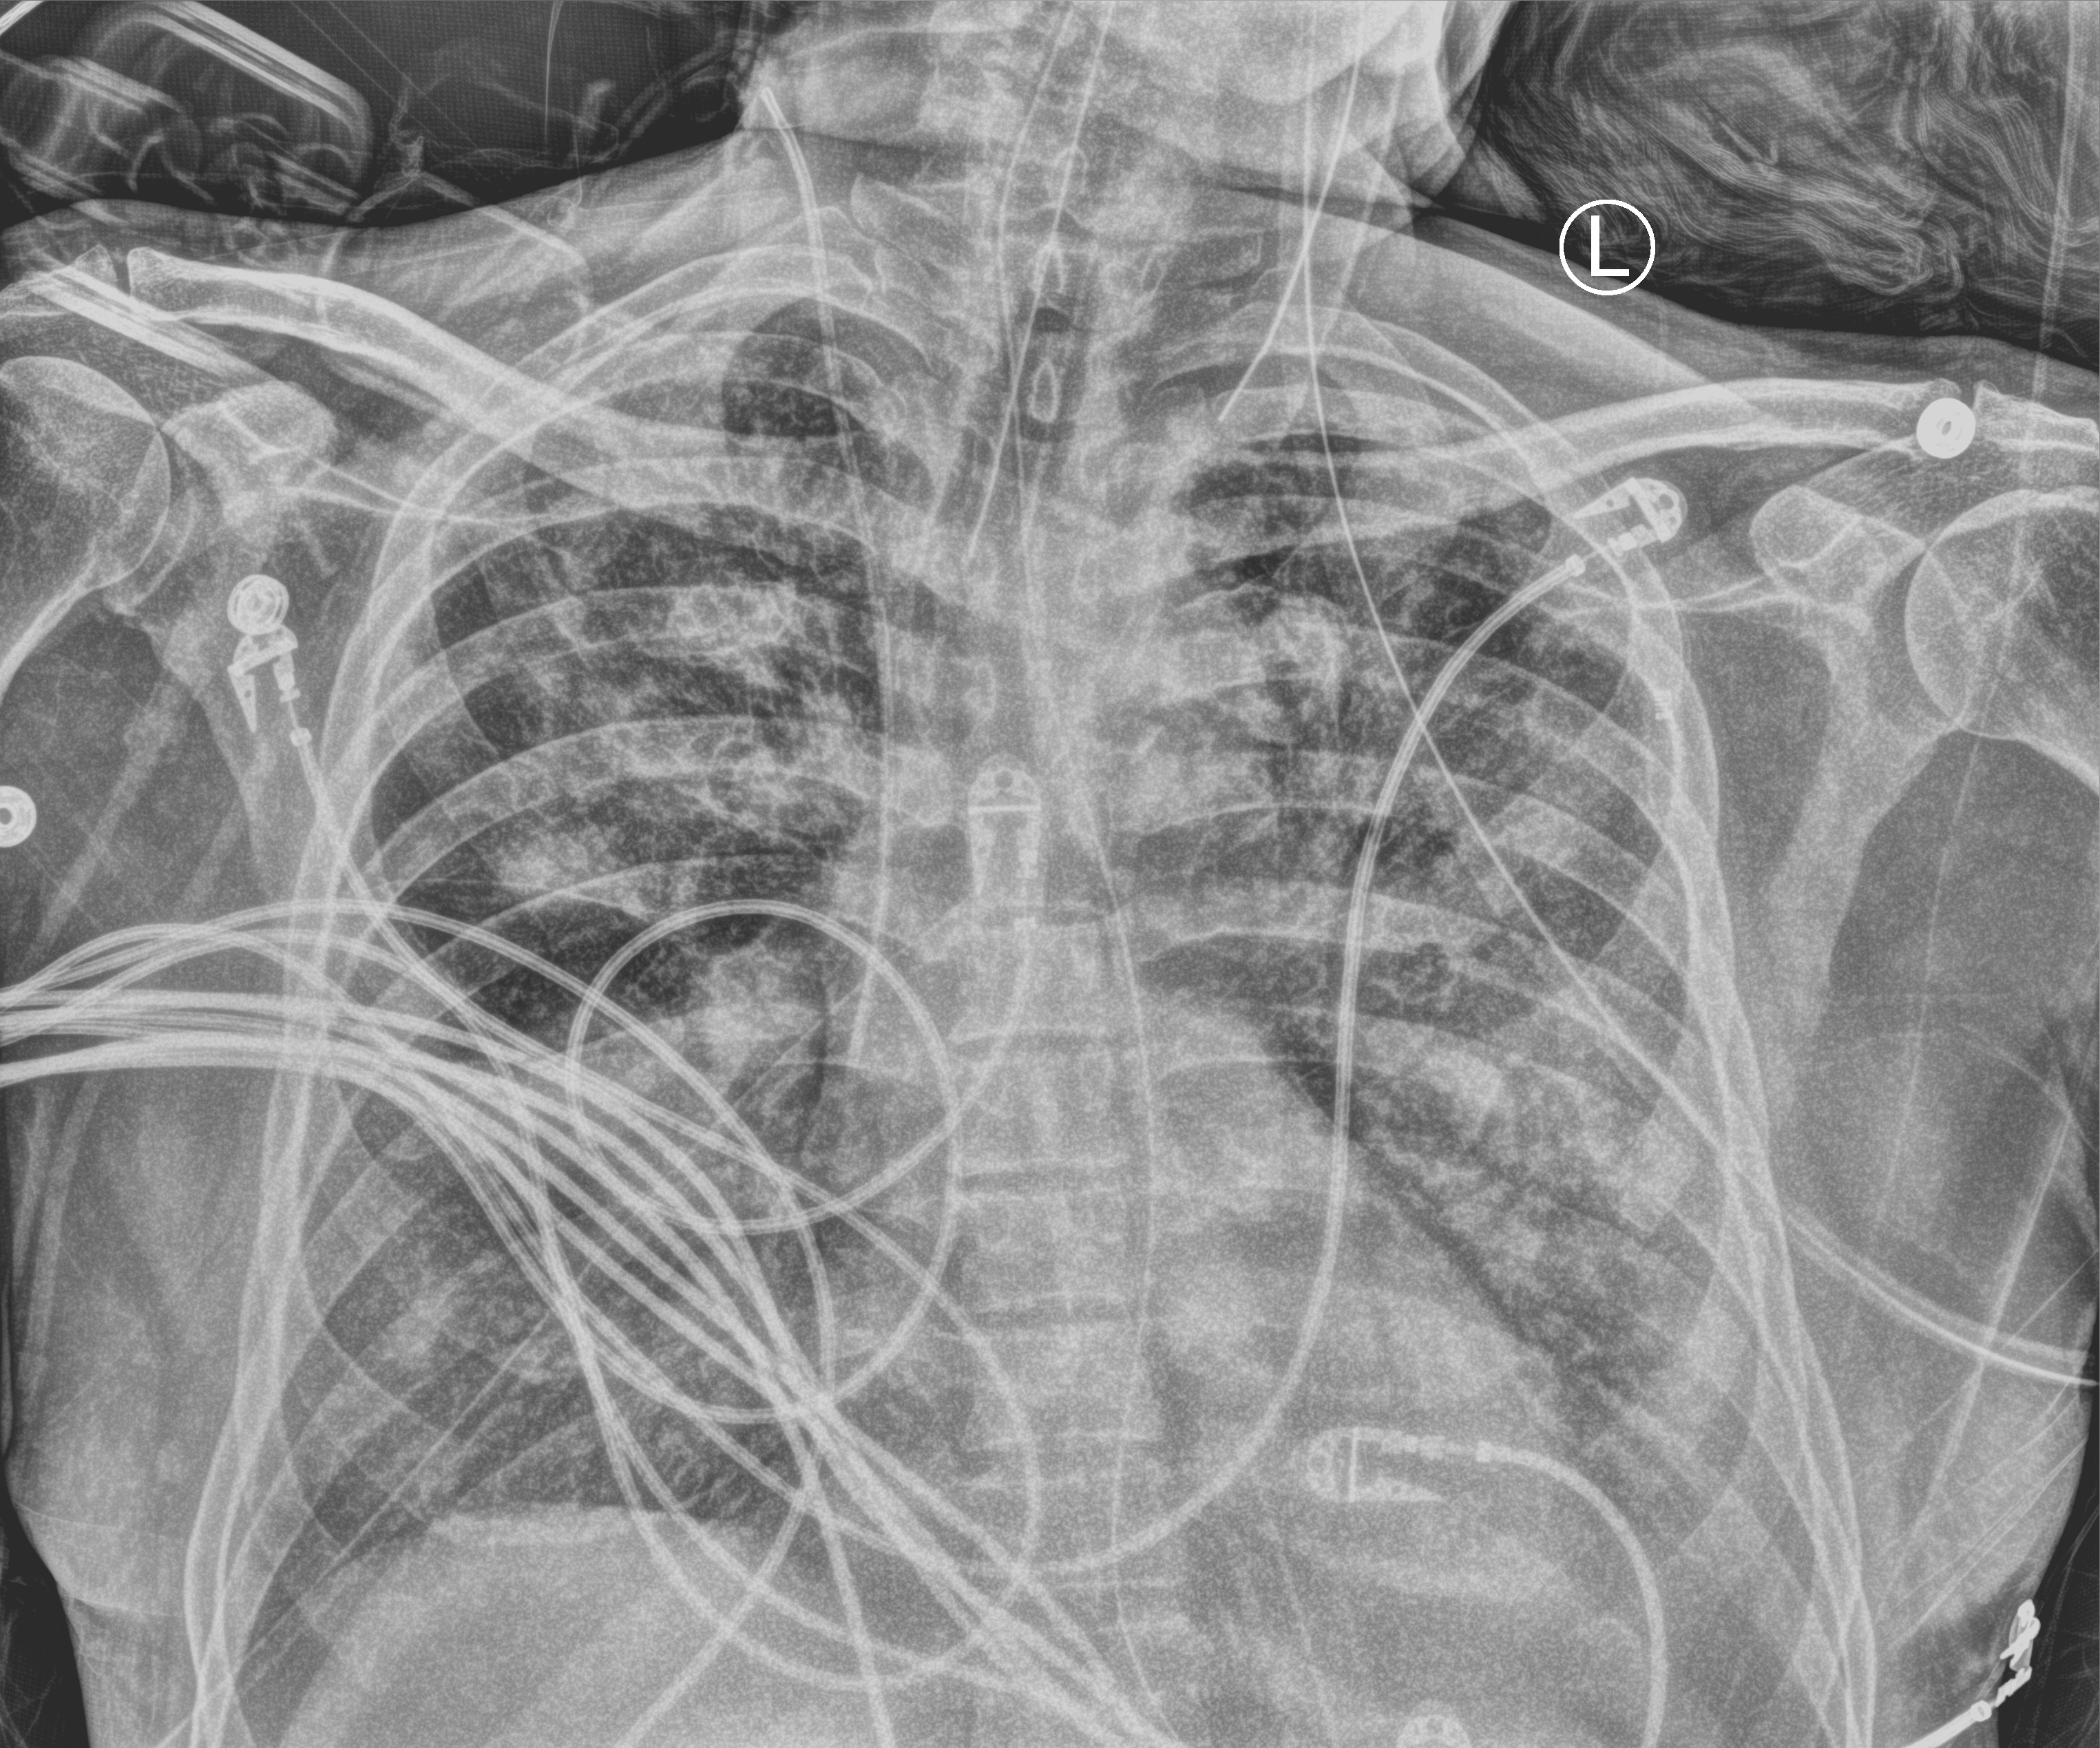
Portable chest radiograph; anteroposterior (AP) projection. Patient hospitalised with COVID-19; male, aged 60–74 years.
Admission-level facts for this patient (not findings on this image; timing relative to this image not recorded): admitted to intensive care during this hospital stay: yes; mechanically ventilated during this hospital stay: yes.